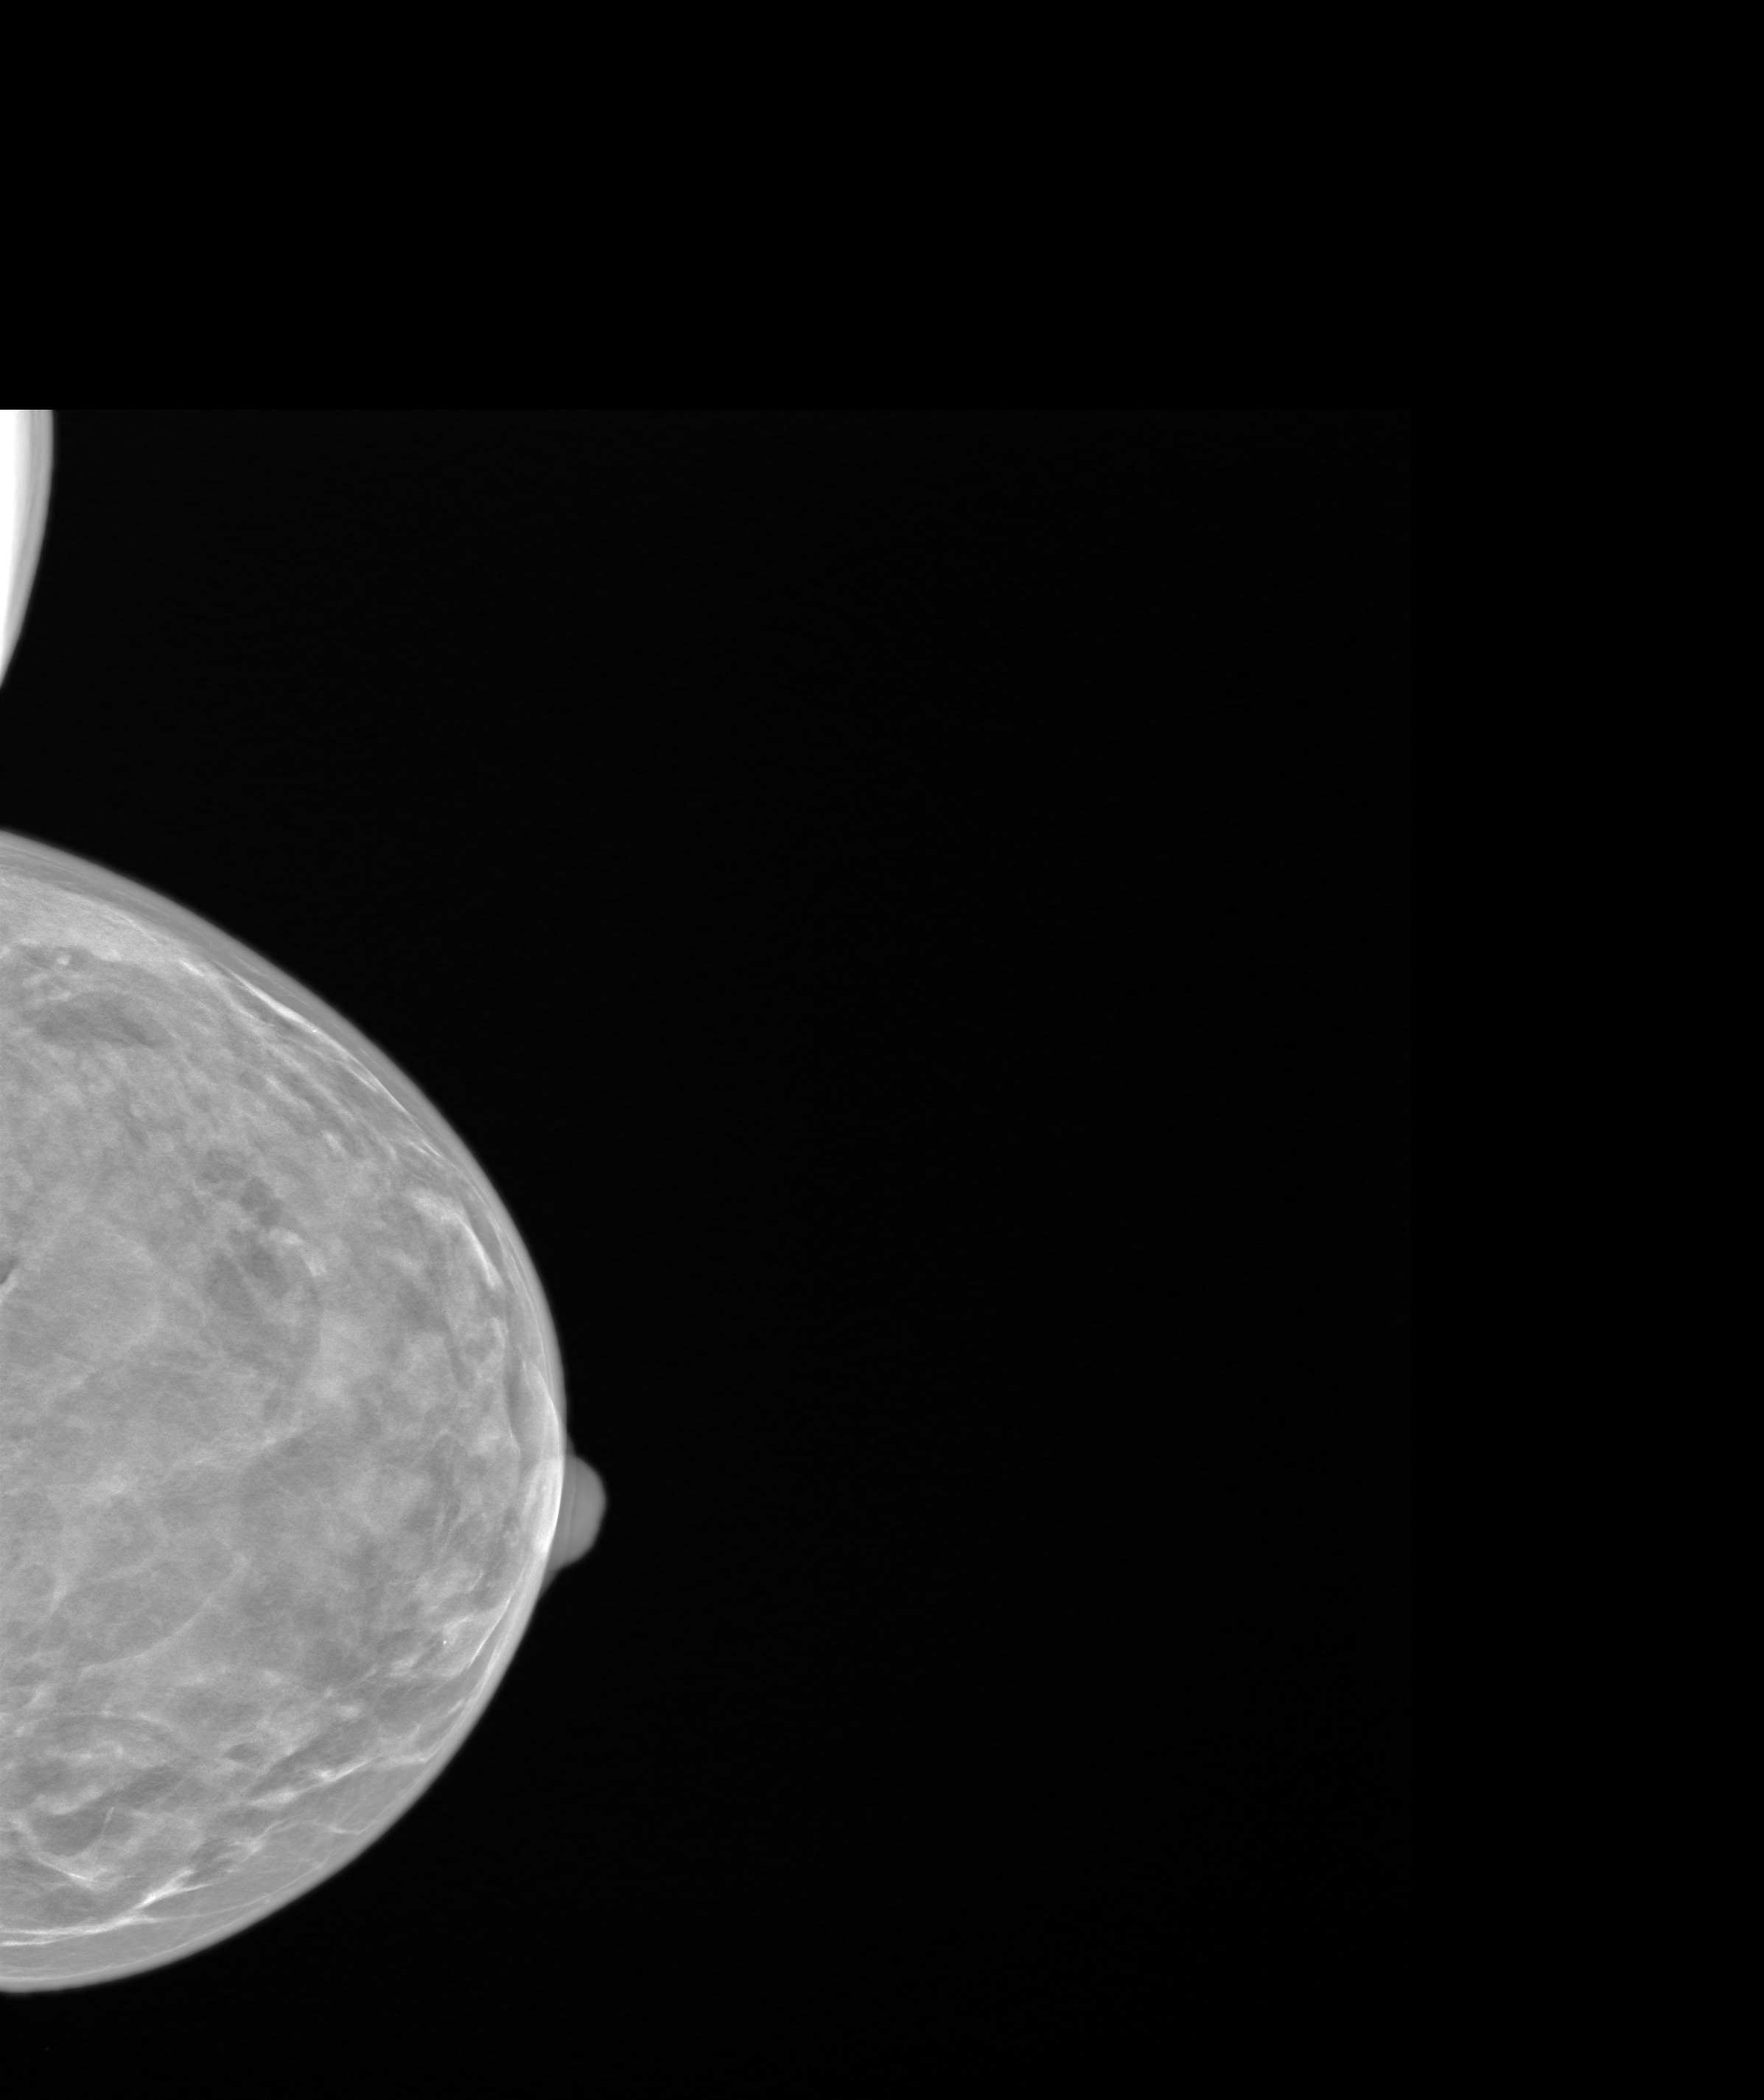
Annual screening mammography examination. Patient: female, 46 years.
Image type: synthesized 2-D view from tomosynthesis. Breast: left. Projection: craniocaudal (CC) view.